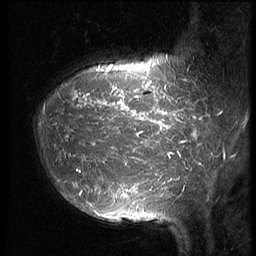
Breast MRI (dynamic contrast-enhanced), one sagittal slice; position 15 of 64 along the scan axis; 3 images stored at this slice position (order not interpretable as contrast timing); 1.5 T; TE 4.2 ms, TR 9 ms; 256 × 256 image matrix, field of view 180 × 180 mm. Female patient, age 39 years. Case-level facts recorded for this patient, not image findings: setting: breast cancer imaged before/during neoadjuvant chemotherapy; receptor status: HER2-positive.
Annotated regions visible in this slice (semi-automatic segmentation, software-assisted and operator-edited):
- analysis volume of interest (the breast-tissue region the enhancement analysis was run in; not a lesion): bounding box <33,47,210,239> (left, top, right, bottom; pixels)
- tumour enhancement mask (voxels above the 140 % enhancement threshold inside the analysis volume of interest): <64,61,209,217>